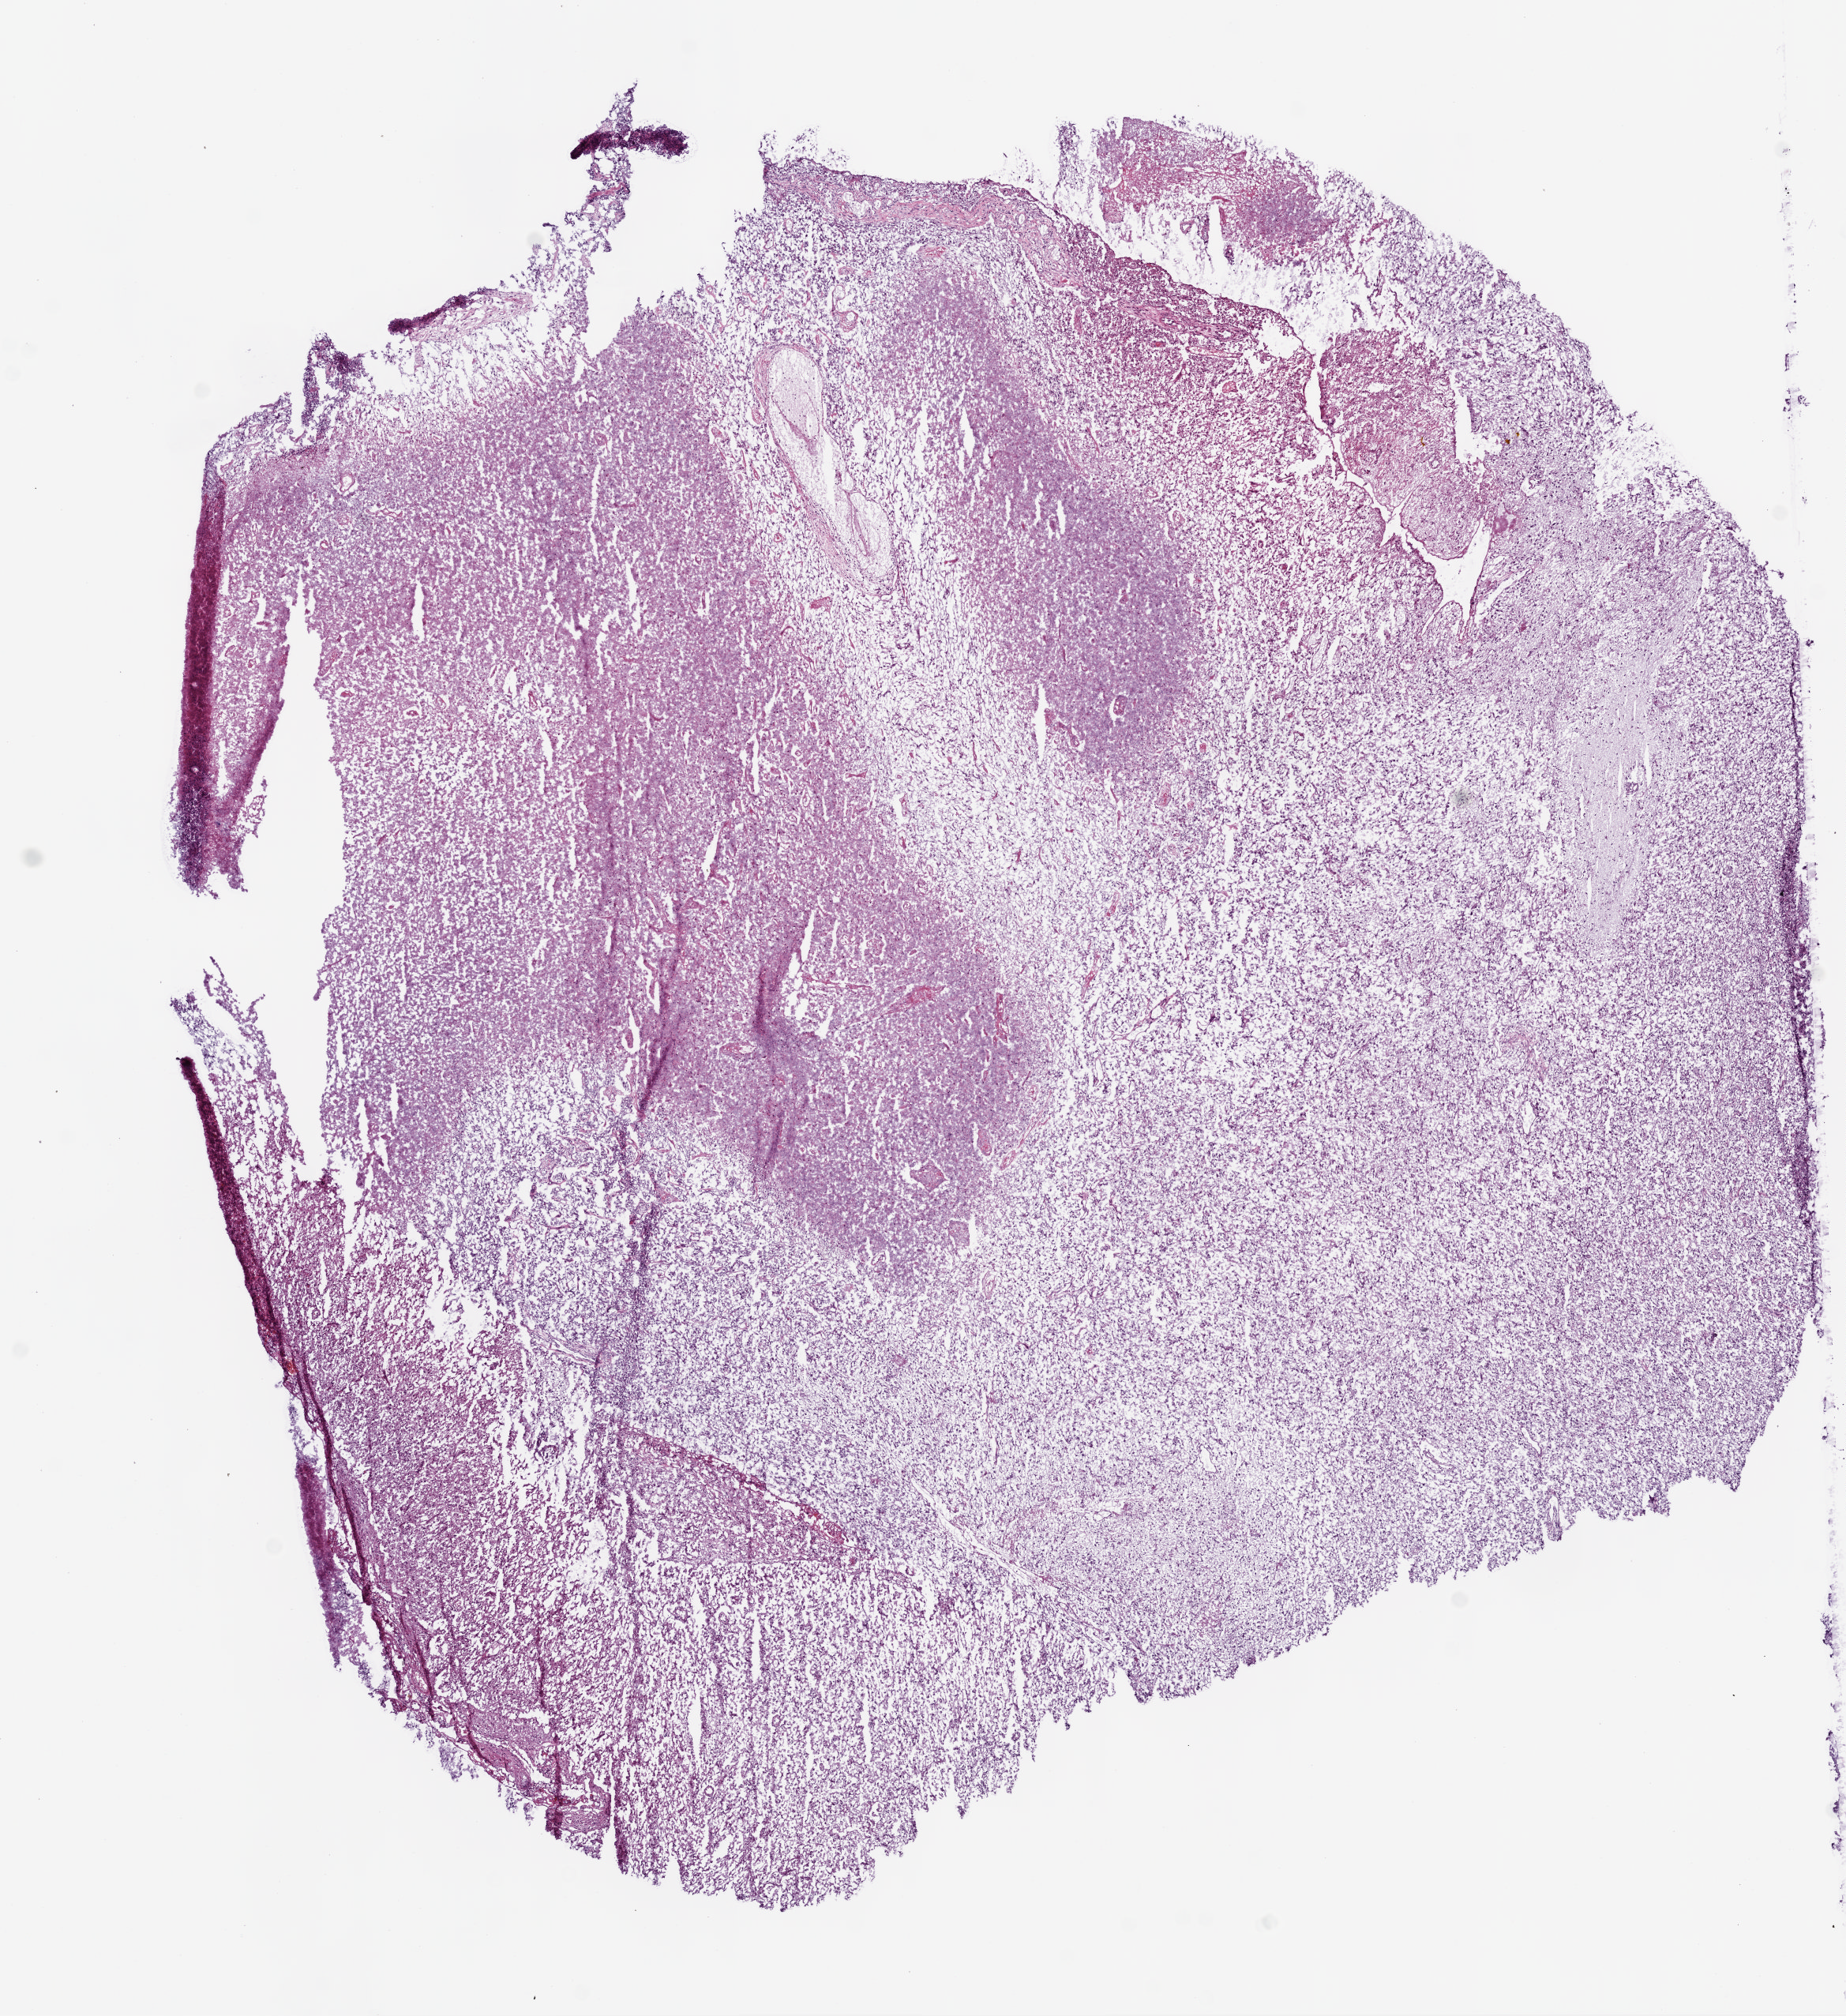
Digitized H&E tissue section (whole slide), low-resolution overview of the scanned area, about 9.4 x 10.2 mm (from a 5x scan); frozen section; sample: primary tumour, brain. Female patient; age at initial diagnosis 78 years. Slide review estimates, as recorded: tumour cells 100%, tumour nuclei 80%, normal cells 0%, stromal cells 0%, necrosis 0%.
Diagnosis: Glioblastoma.